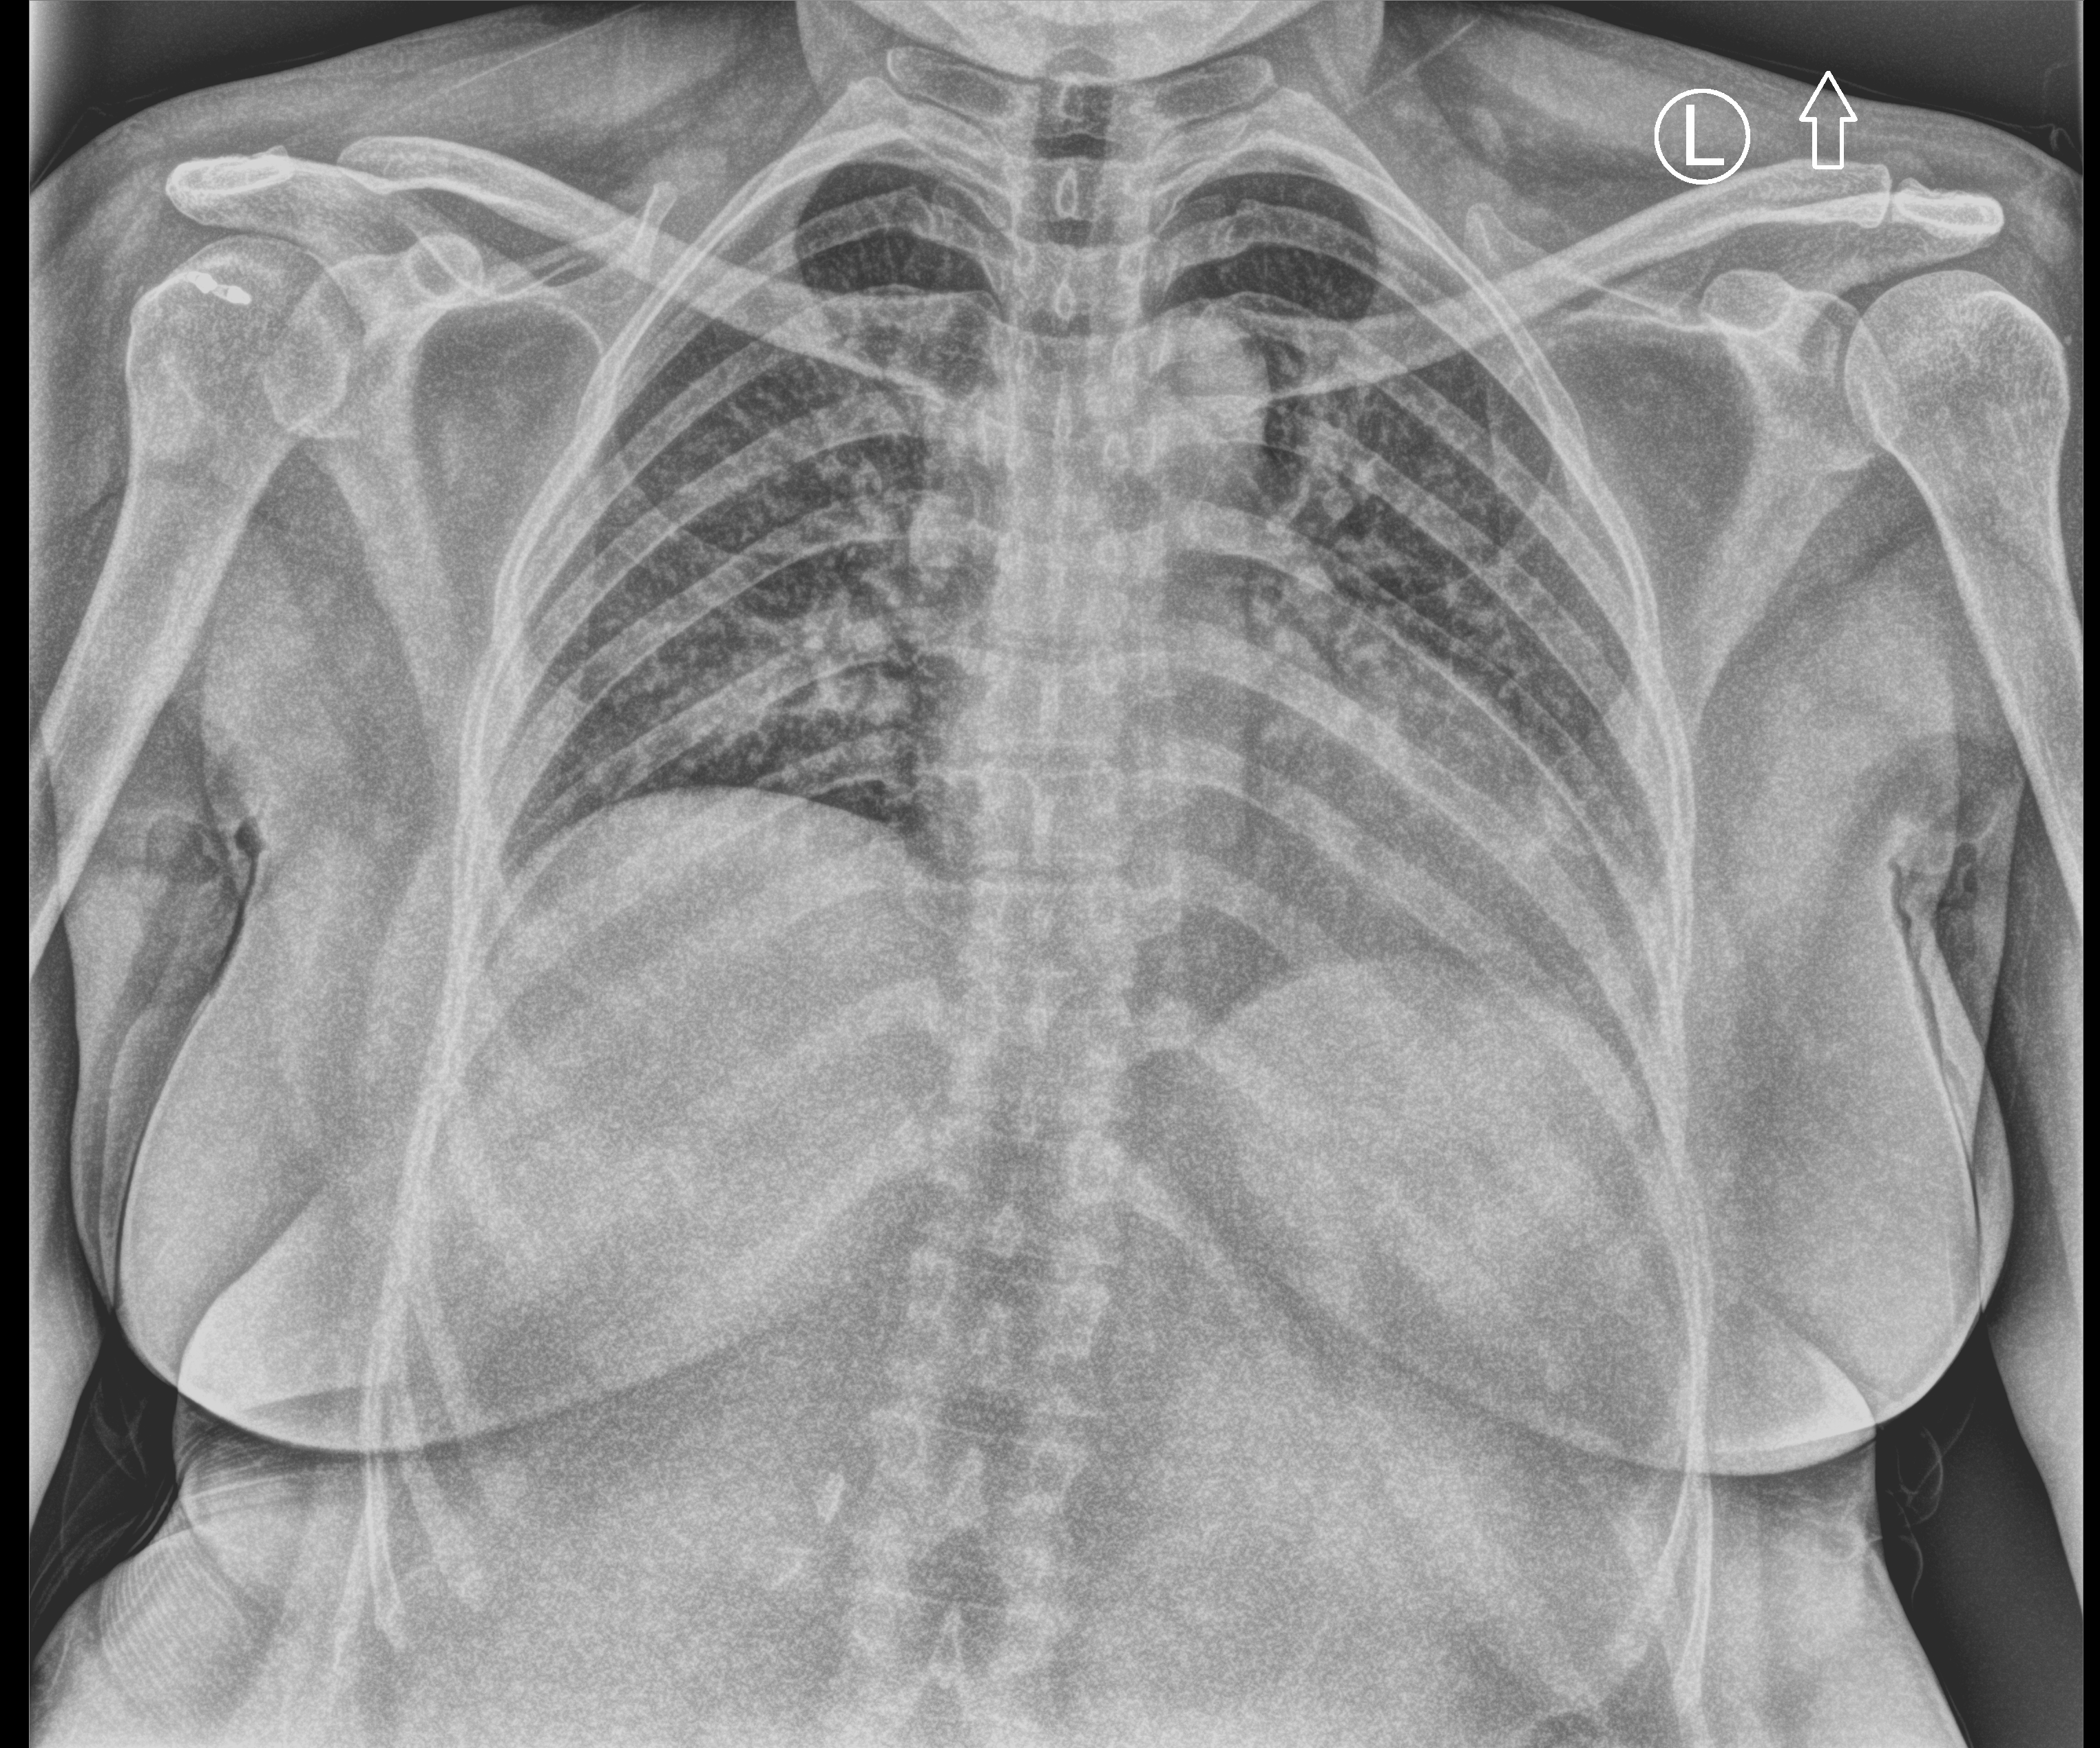
Chest X-ray (portable), anteroposterior (AP) projection. Female patient hospitalised with COVID-19, age 18–59 years.
Admission-level facts for this patient (not findings on this image; timing relative to this image not recorded): admitted to intensive care during this hospital stay: no.